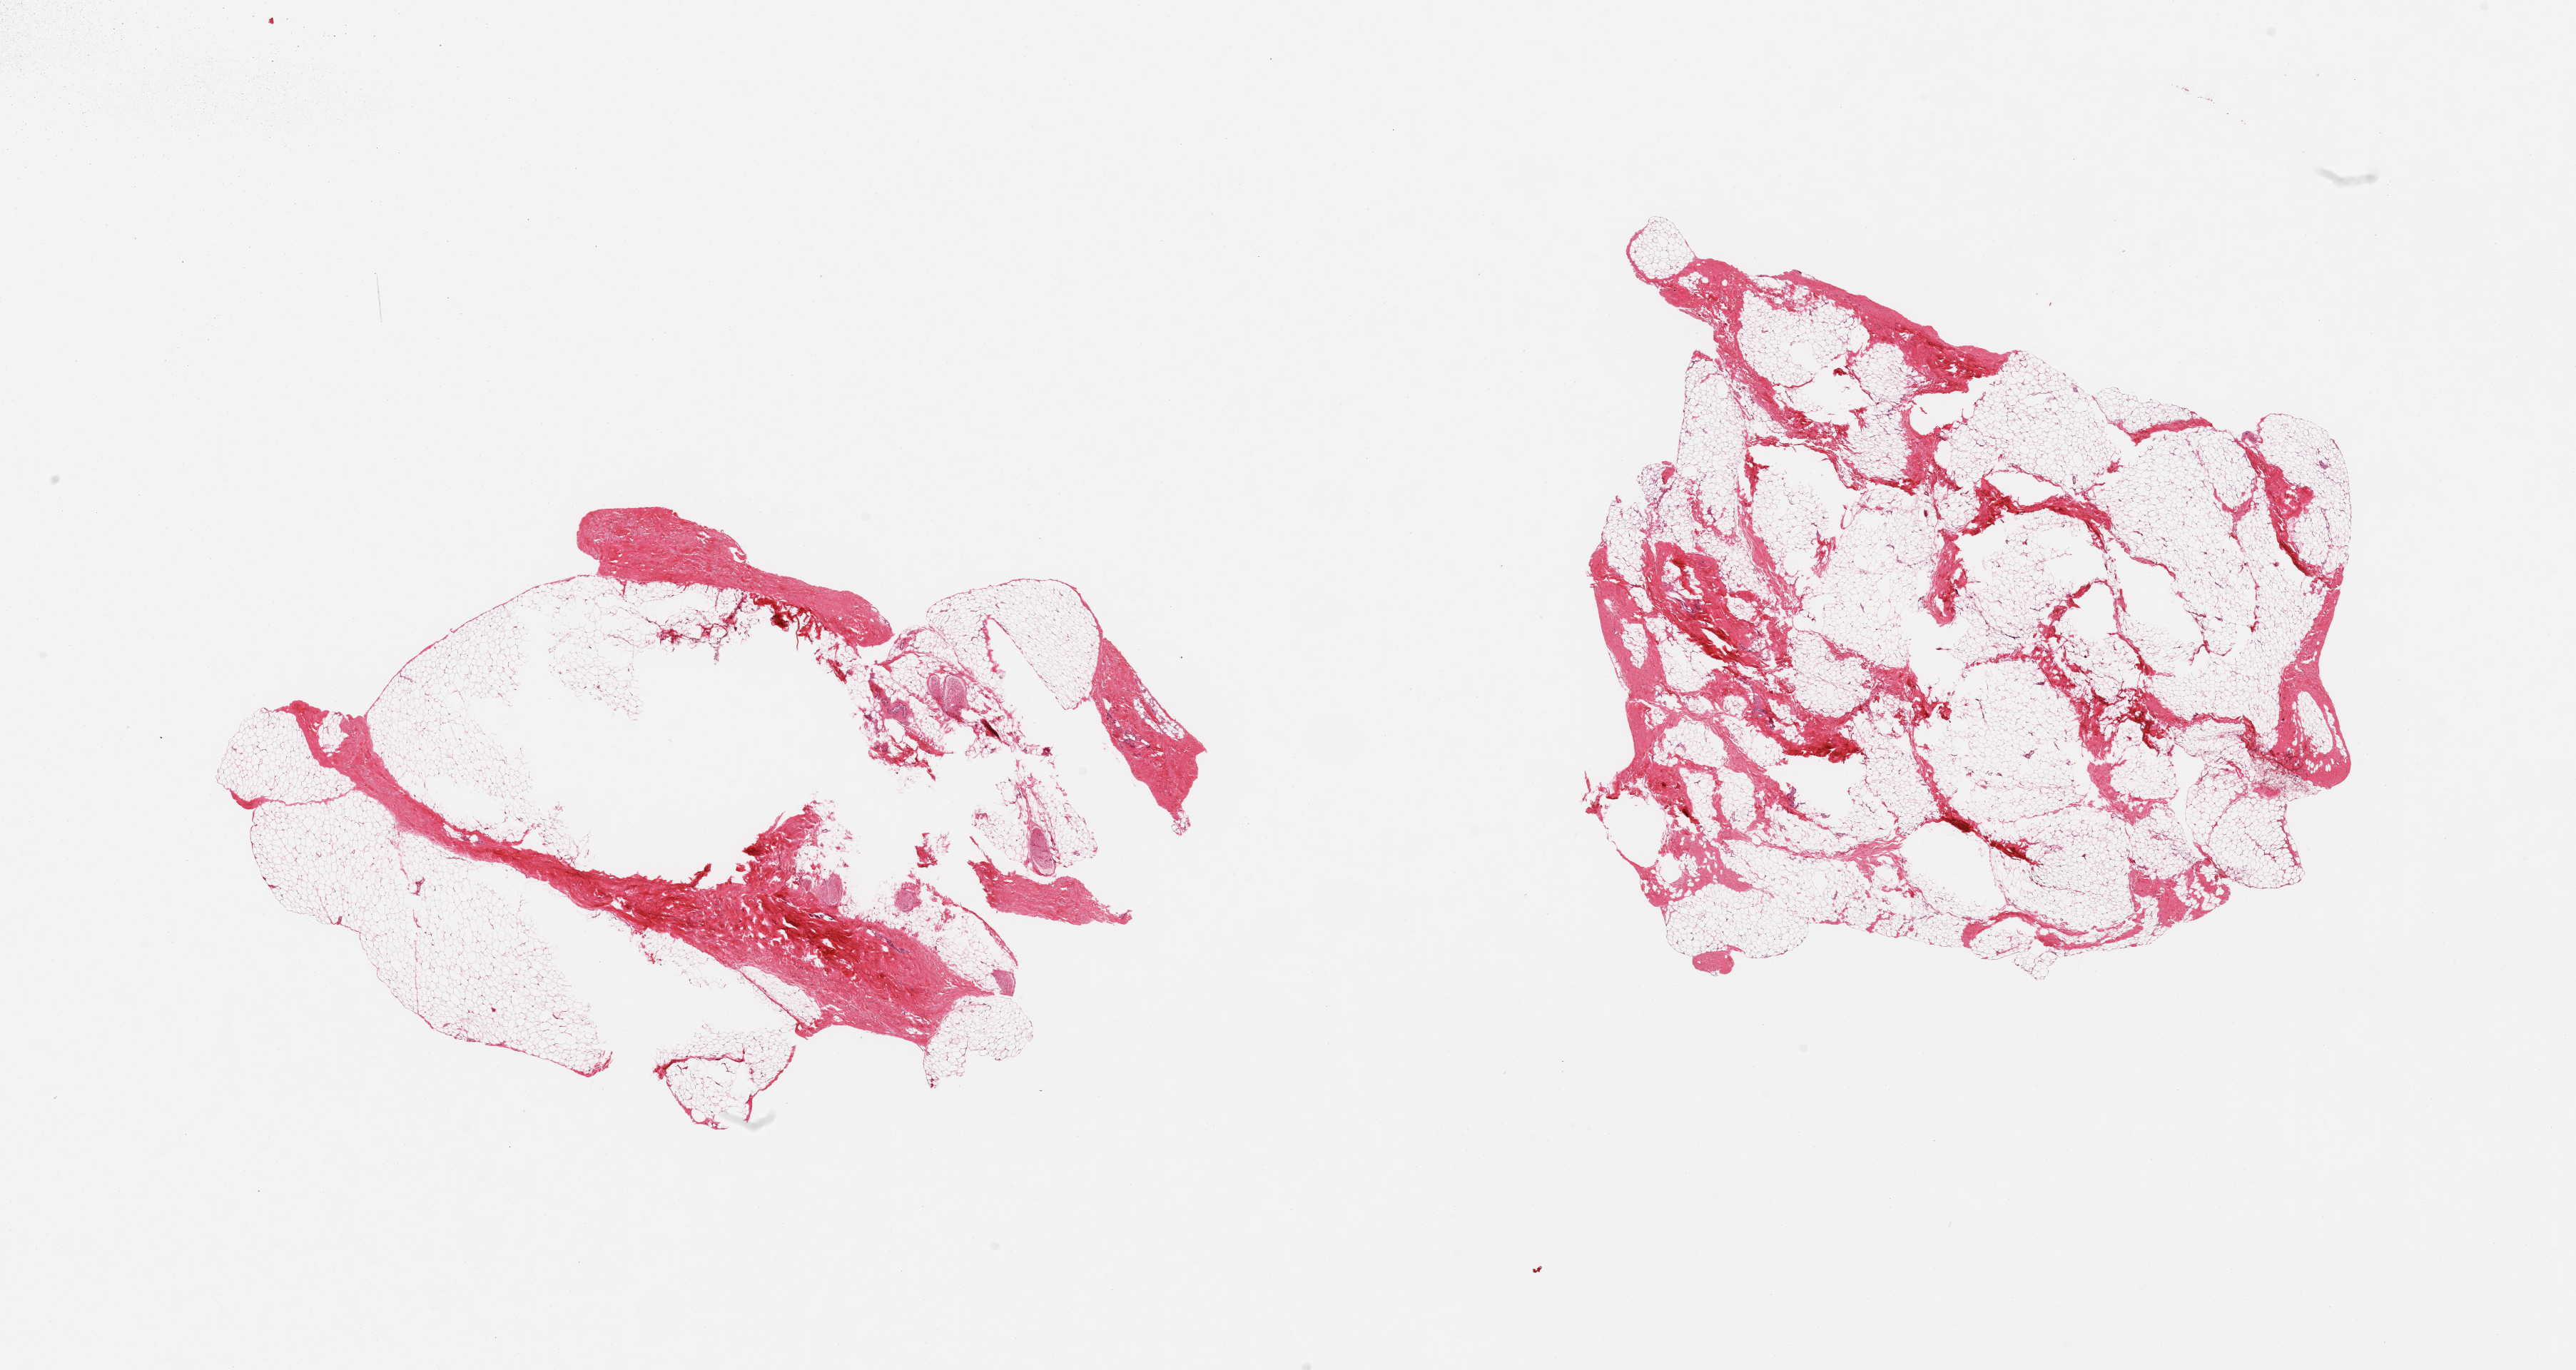
Digitized haematoxylin and eosin-stained section — a low-resolution overview of the entire scanned area, about 28.5 x 15.2 mm; PAXgene-fixed paraffin-embedded (PFPE) section; sampled site (target tissue): breast; tissue donor sample. Donor sex: male.
- review note (as recorded): 2 pieces; predominantly fat with 10-20% interspersed fibrous tissue and nerve, no ductal elements in this section, central defect in one piece (?poor fixation)